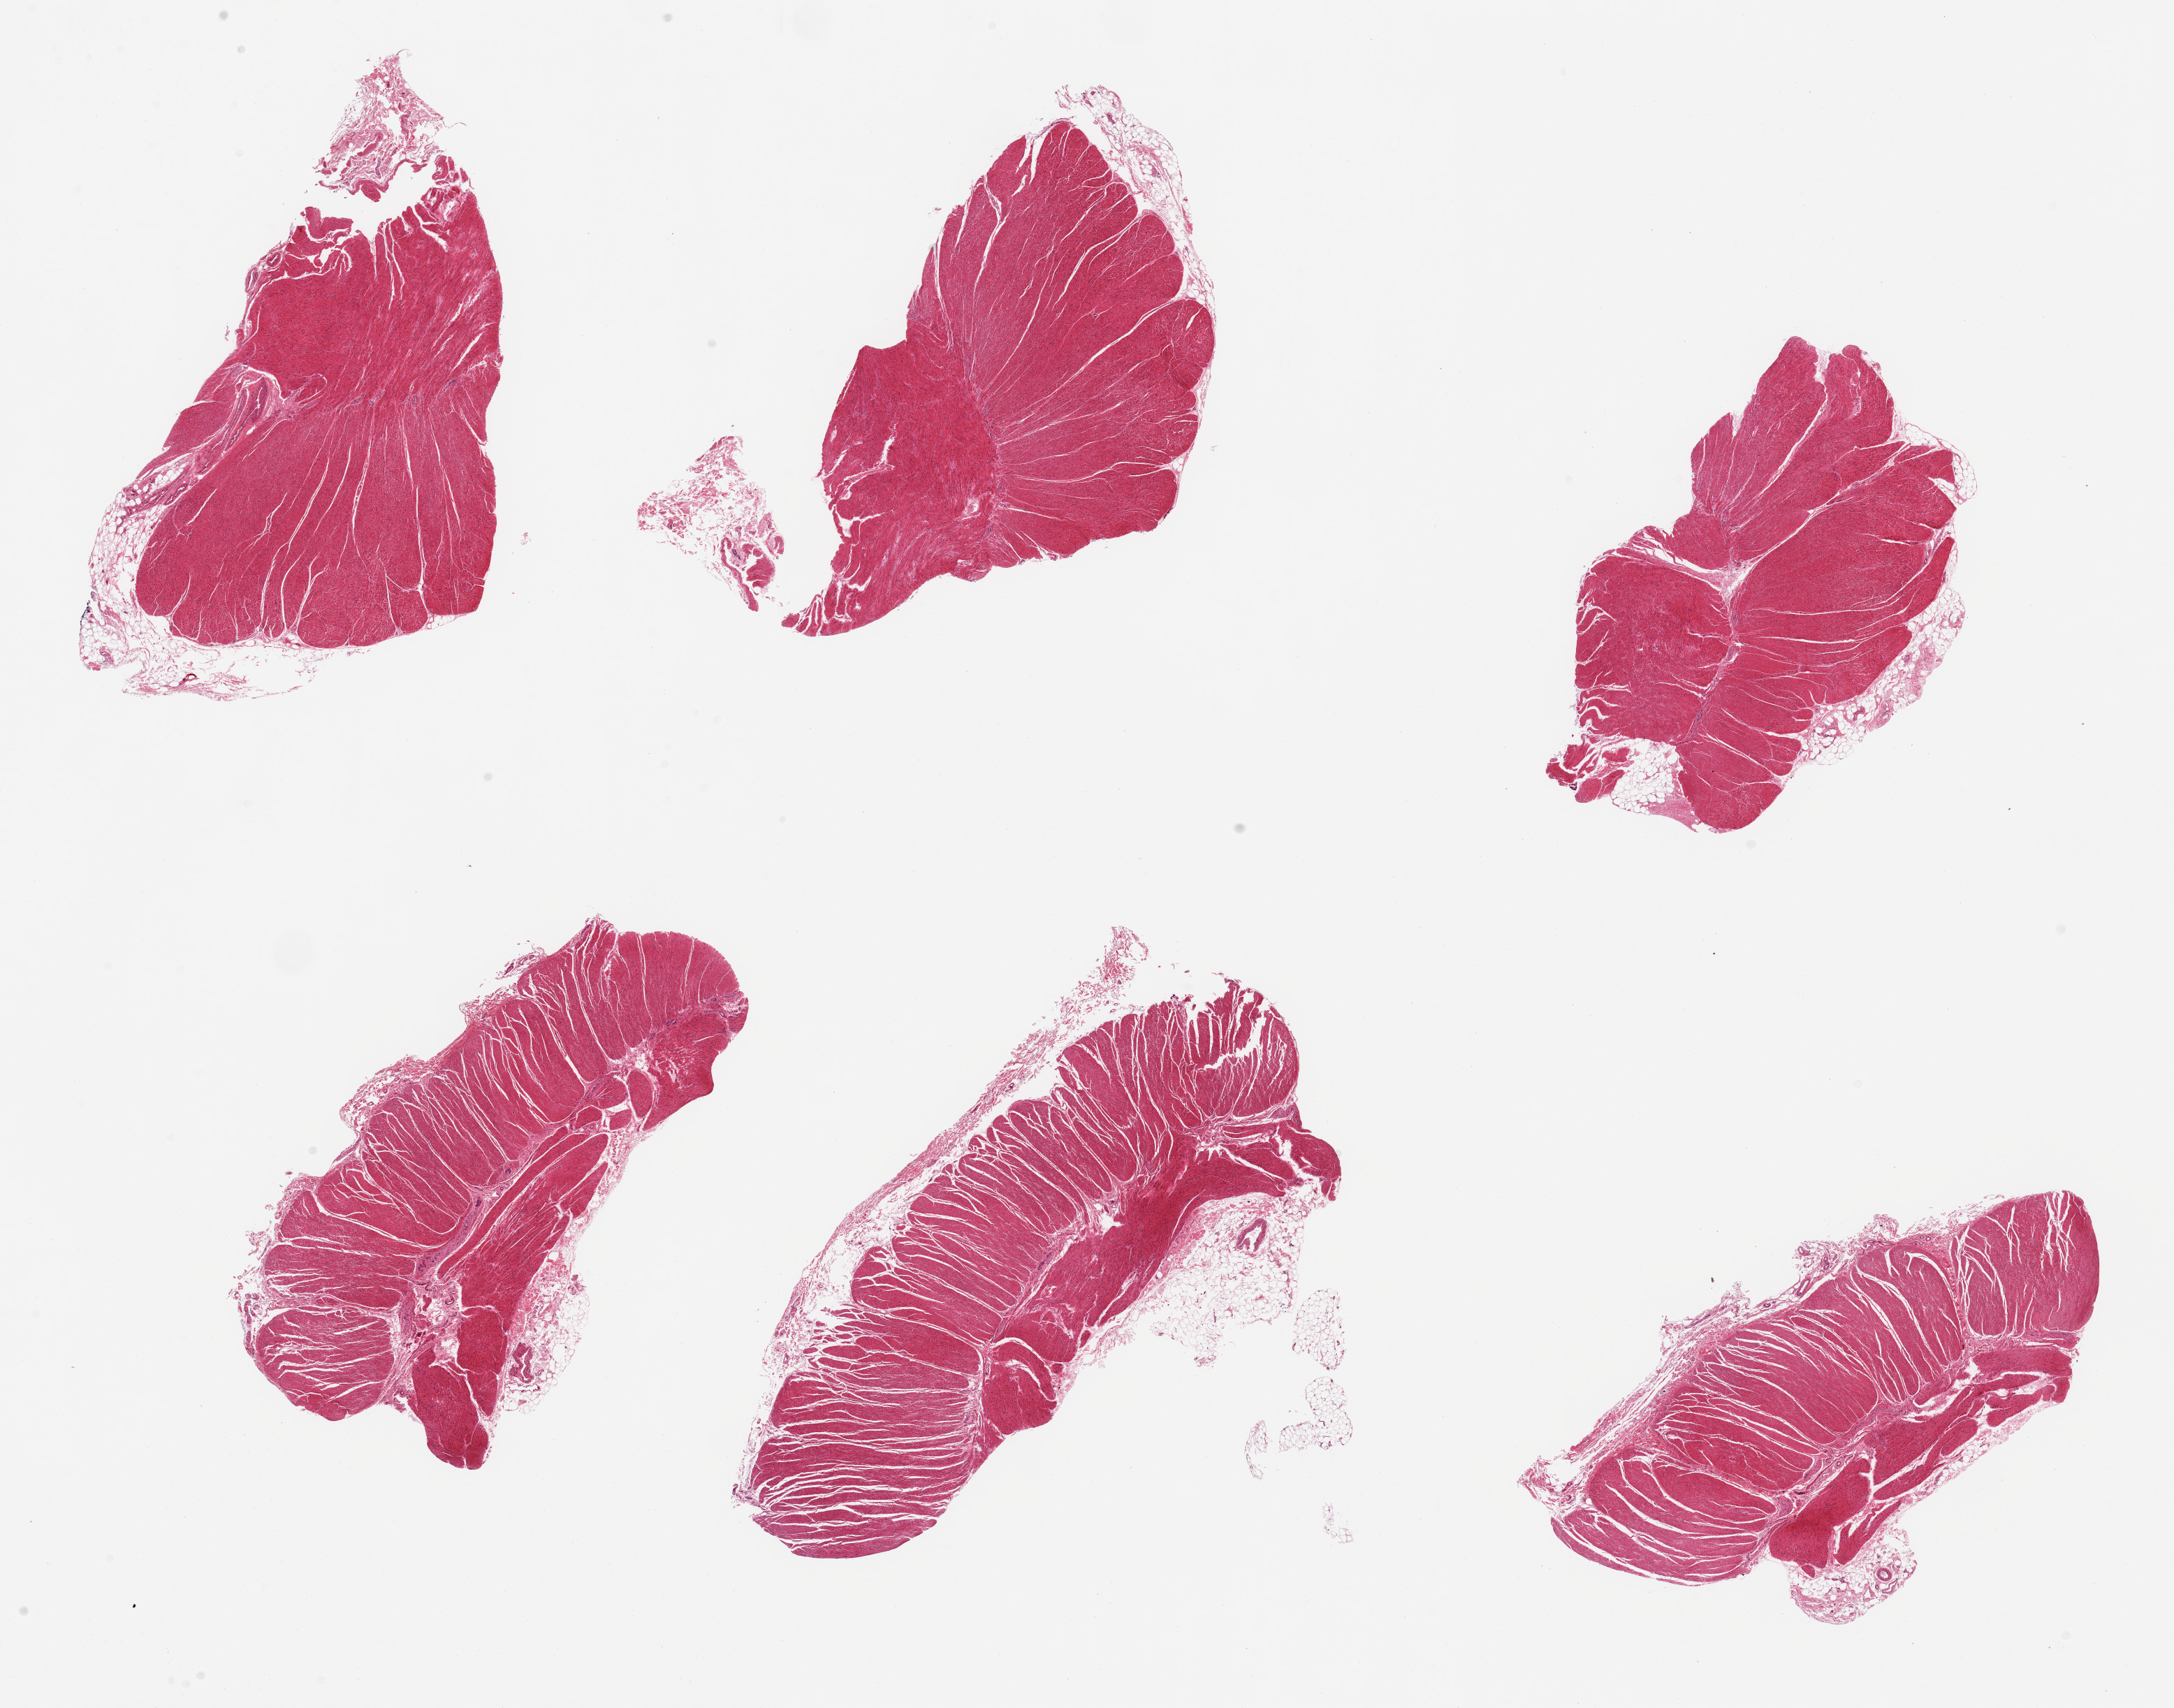
H&E whole-slide image, a low-resolution overview of the entire scanned area, about 24.6 x 19.3 mm, PAXgene-fixed paraffin-embedded (PFPE) section, target tissue: sigmoid colon, donor tissue sample. Donor sex: female.
Reviewer comment on this tissue sample: 6 pieces, all target muscularis.